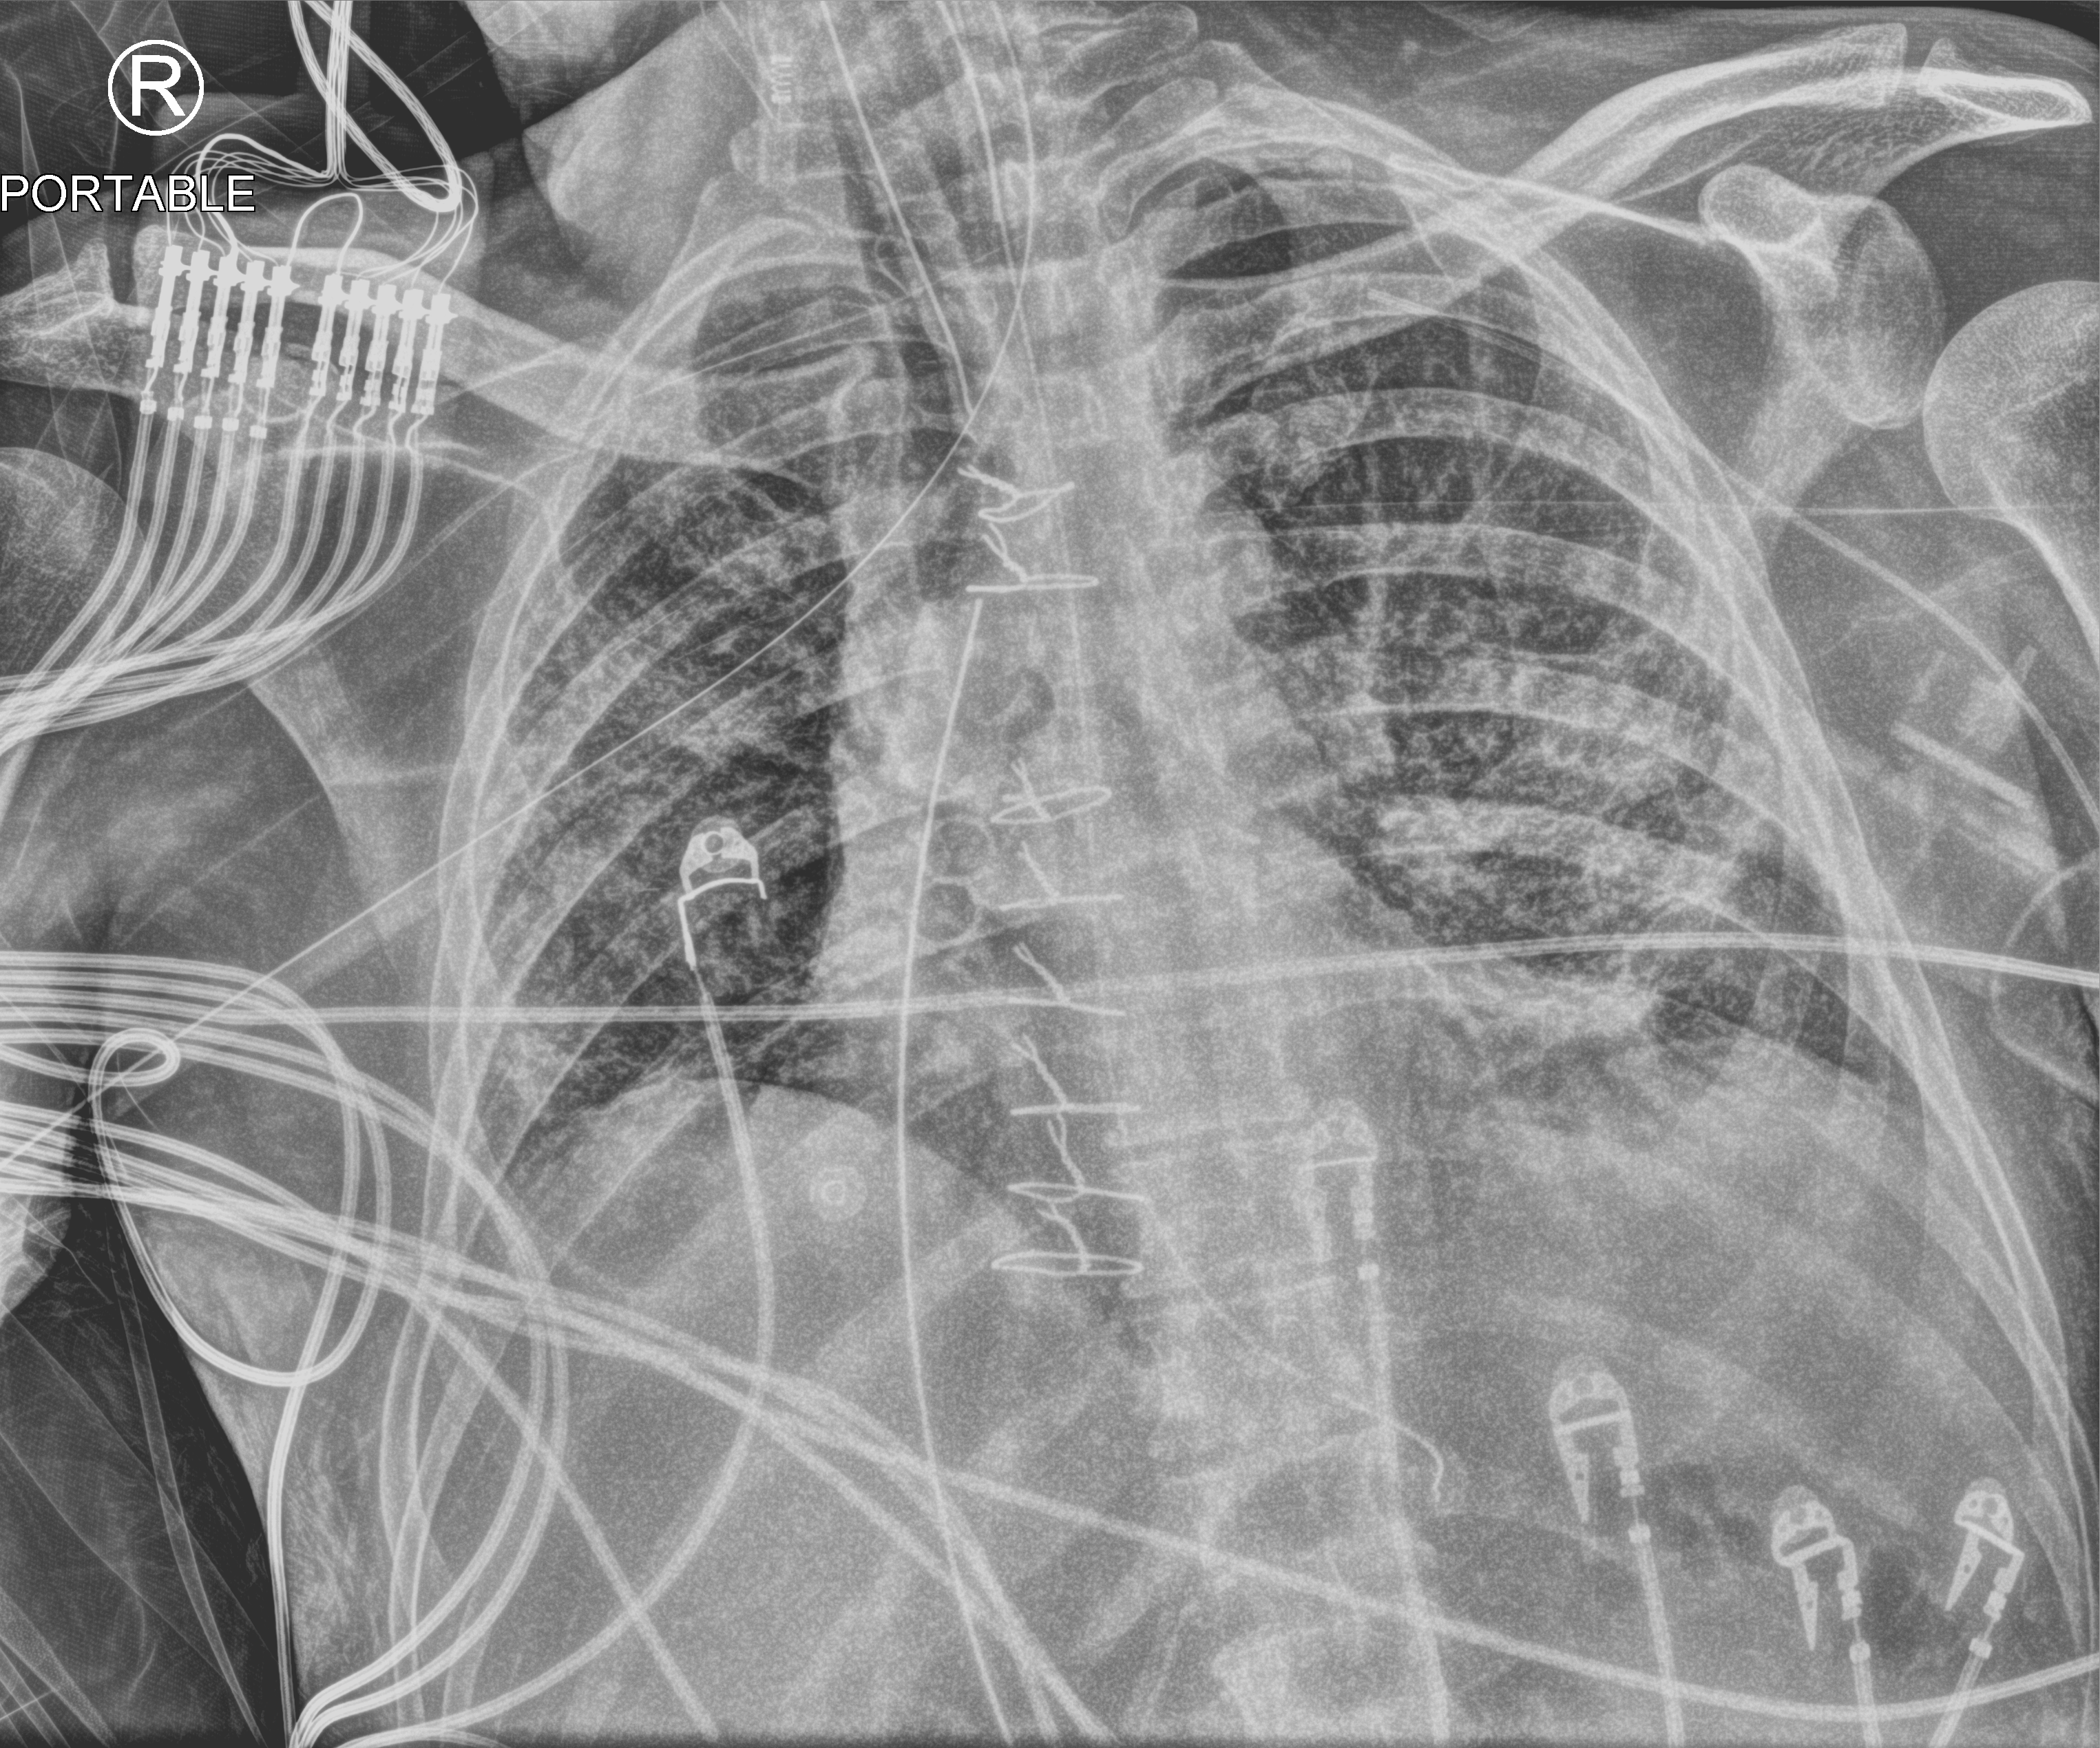
Chest X-ray (portable). Male patient hospitalised with COVID-19, age 18–59 years.
Hospital-stay facts (about this admission, not read from this image; timing relative to this image not recorded):
- COPD (admission record): yes
- hypertension (admission record): no